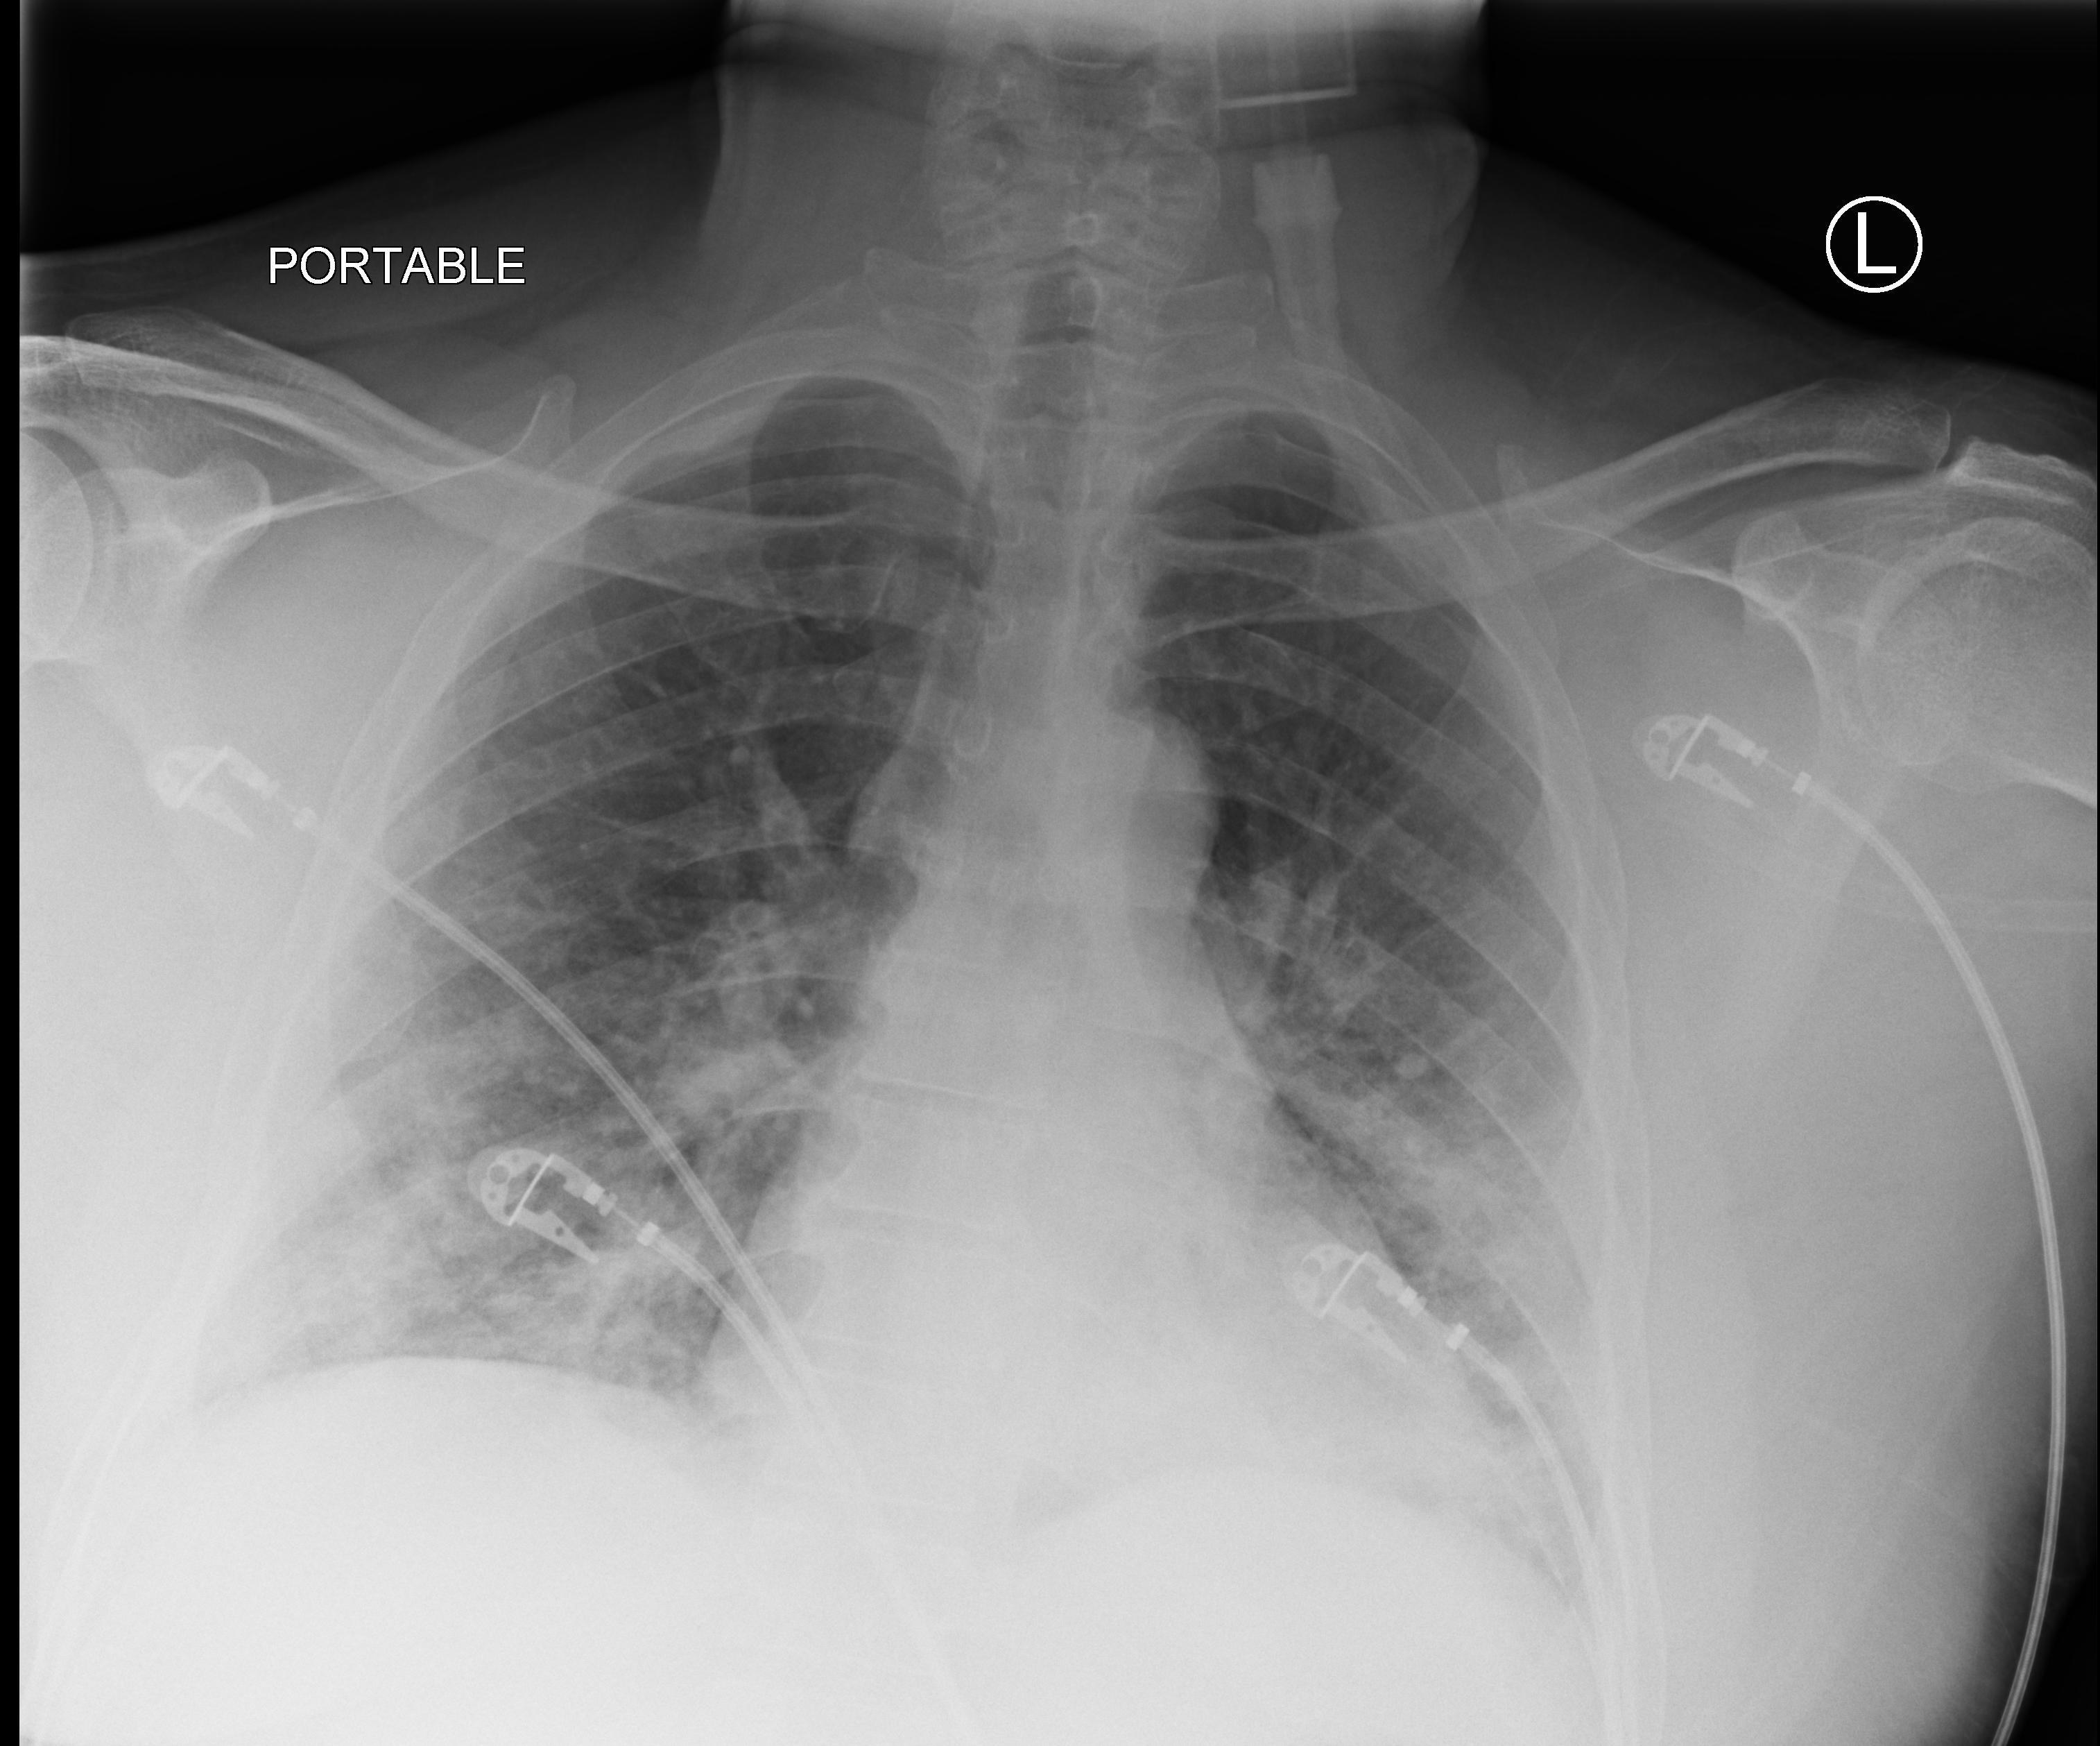
Chest X-ray (portable); anteroposterior (AP) projection. Male patient hospitalised with COVID-19, age 18–59 years.
Hospital-stay facts (about this admission, not read from this image; timing relative to this image not recorded): mechanically ventilated during this hospital stay: yes.